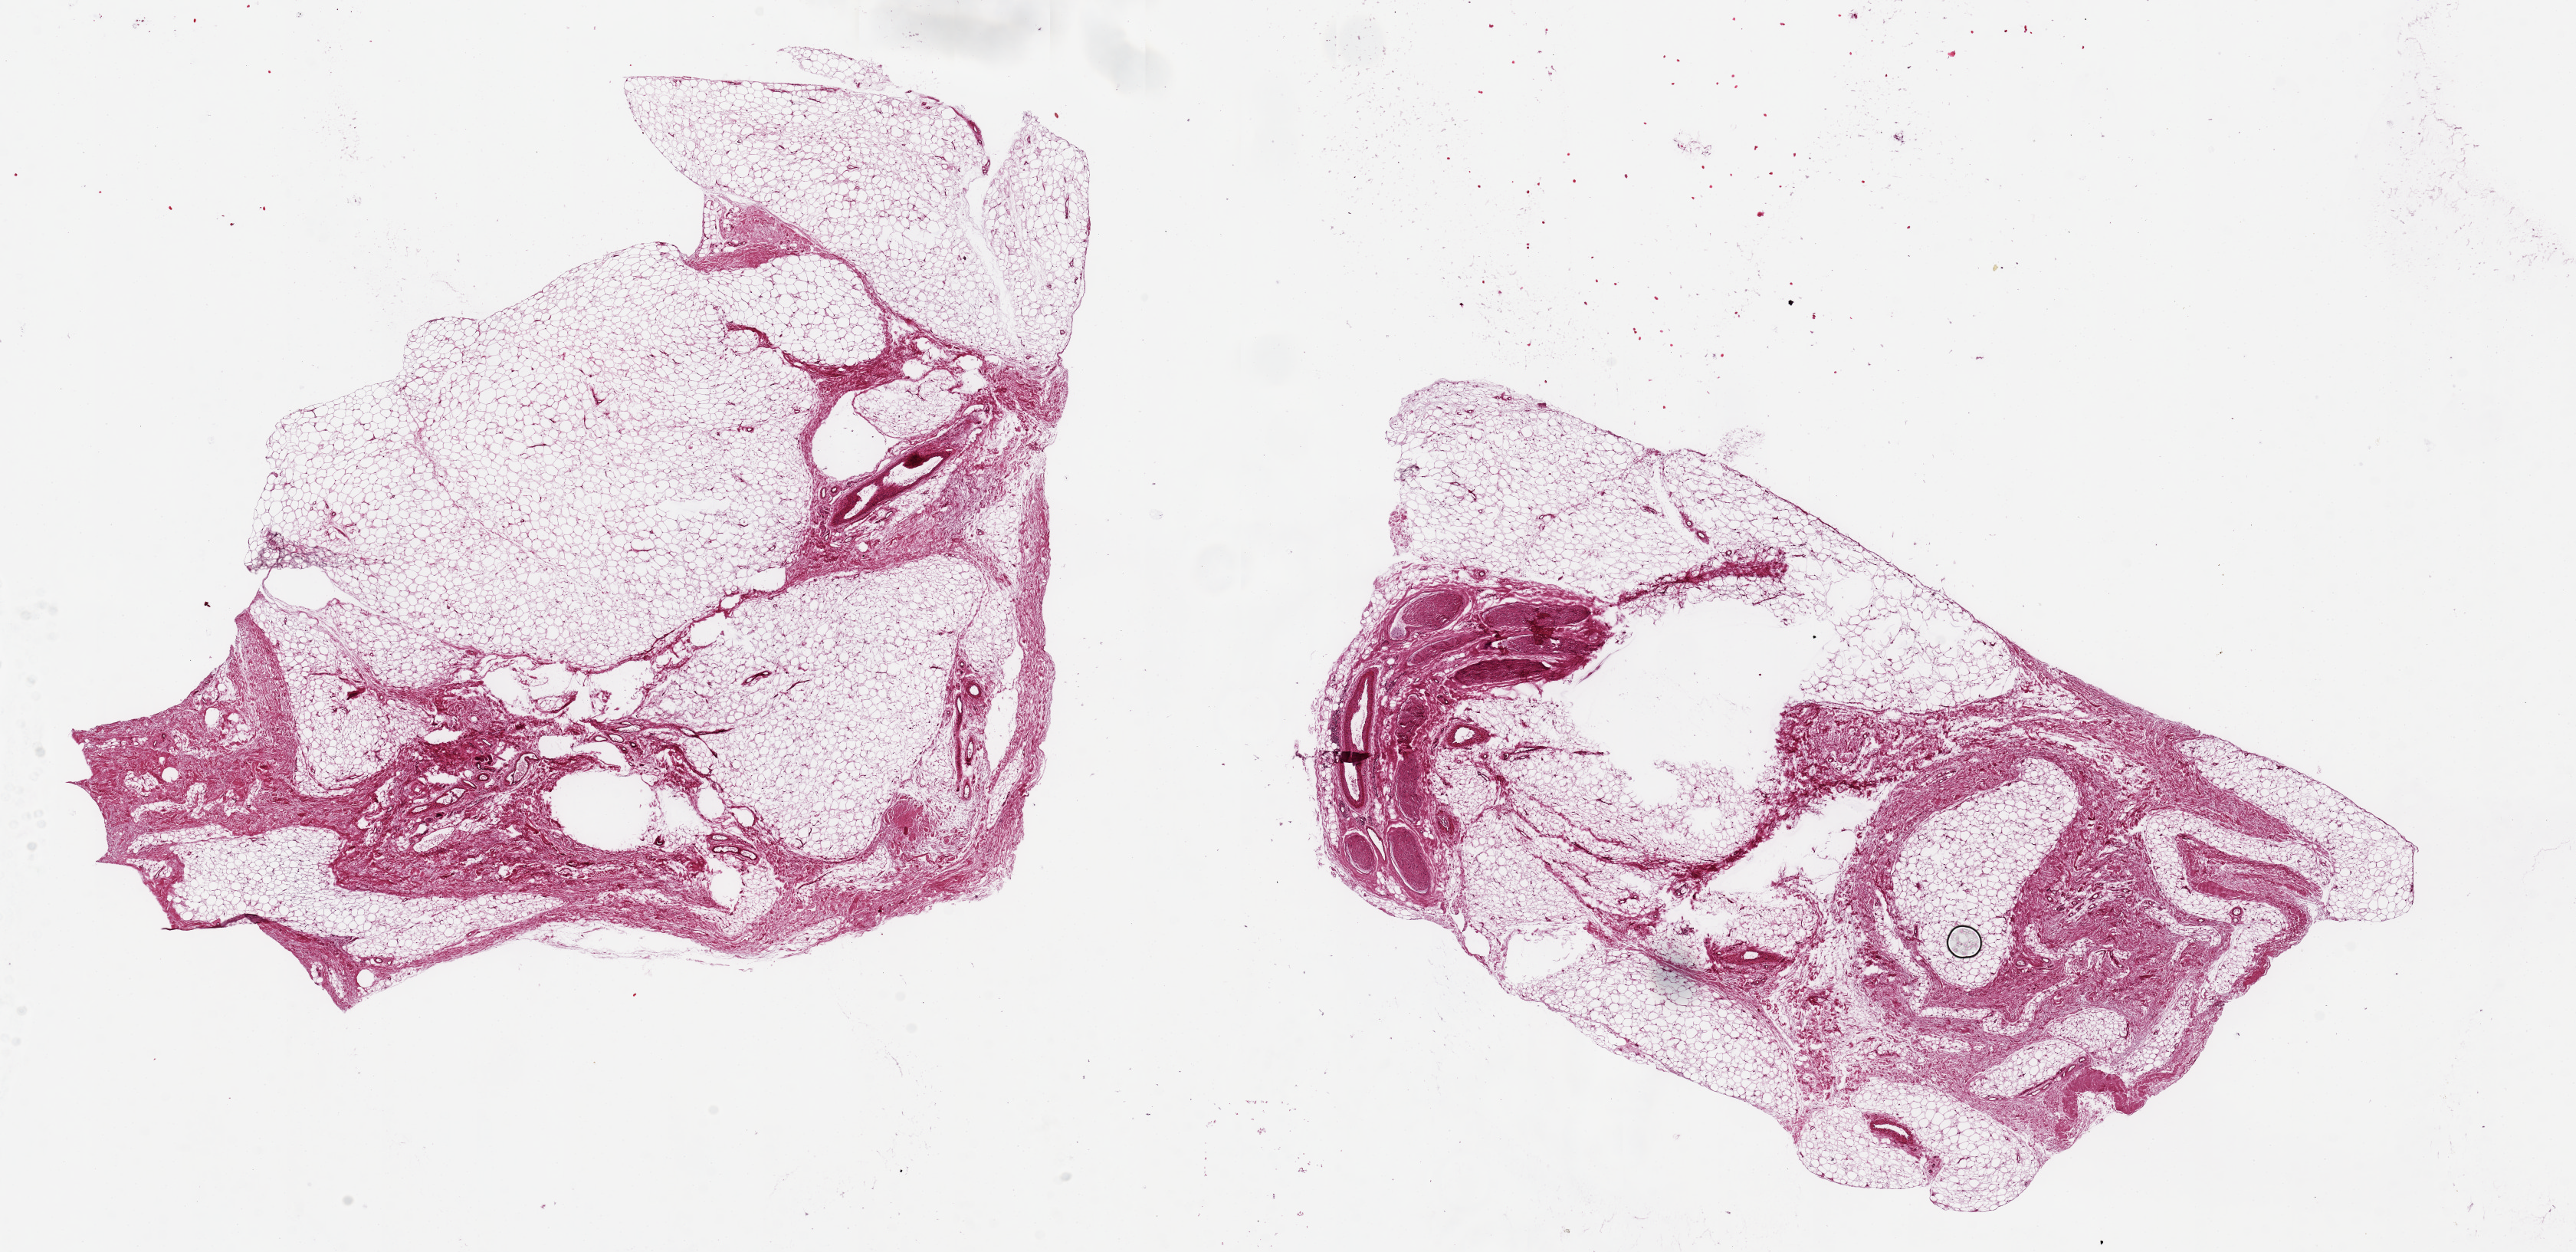
Digitized H&E-stained section — low-resolution overview of the scanned area, about 26.6 x 12.9 mm (acquisition: 20x scan), PAXgene-fixed paraffin-embedded (PFPE) section, section of adipose tissue (target tissue), donor tissue sample. Donor: male.
Review note (as recorded): pieces 10x5 & 11x9 mm; adipose tissue and an embedded 3x1 mm nerve.